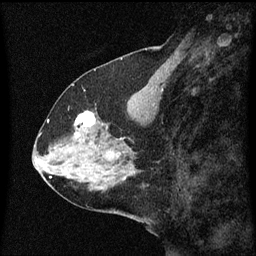
Breast MRI (dynamic contrast-enhanced), one sagittal slice; slice 26 of 60 in the series (ordered by position); dynamic contrast-enhanced series, image 2 of 3 at this slice position (ordered by acquisition); 1.5 T; TE 4.2 ms, TR 8.4 ms; 2 mm slice thickness; 256 × 256 image matrix, field of view 200 × 200 mm. Female patient, age 59 years.
Outlined on this slice (semi-automatically segmented with operator editing):
- analysis volume of interest (the breast-tissue region the enhancement analysis was run in; not a lesion): bounding box [x1, y1, x2, y2] px = [73, 112, 99, 137]
- tumour enhancement mask (voxels above the 70 % enhancement threshold inside the analysis volume of interest): [76, 112, 97, 127]